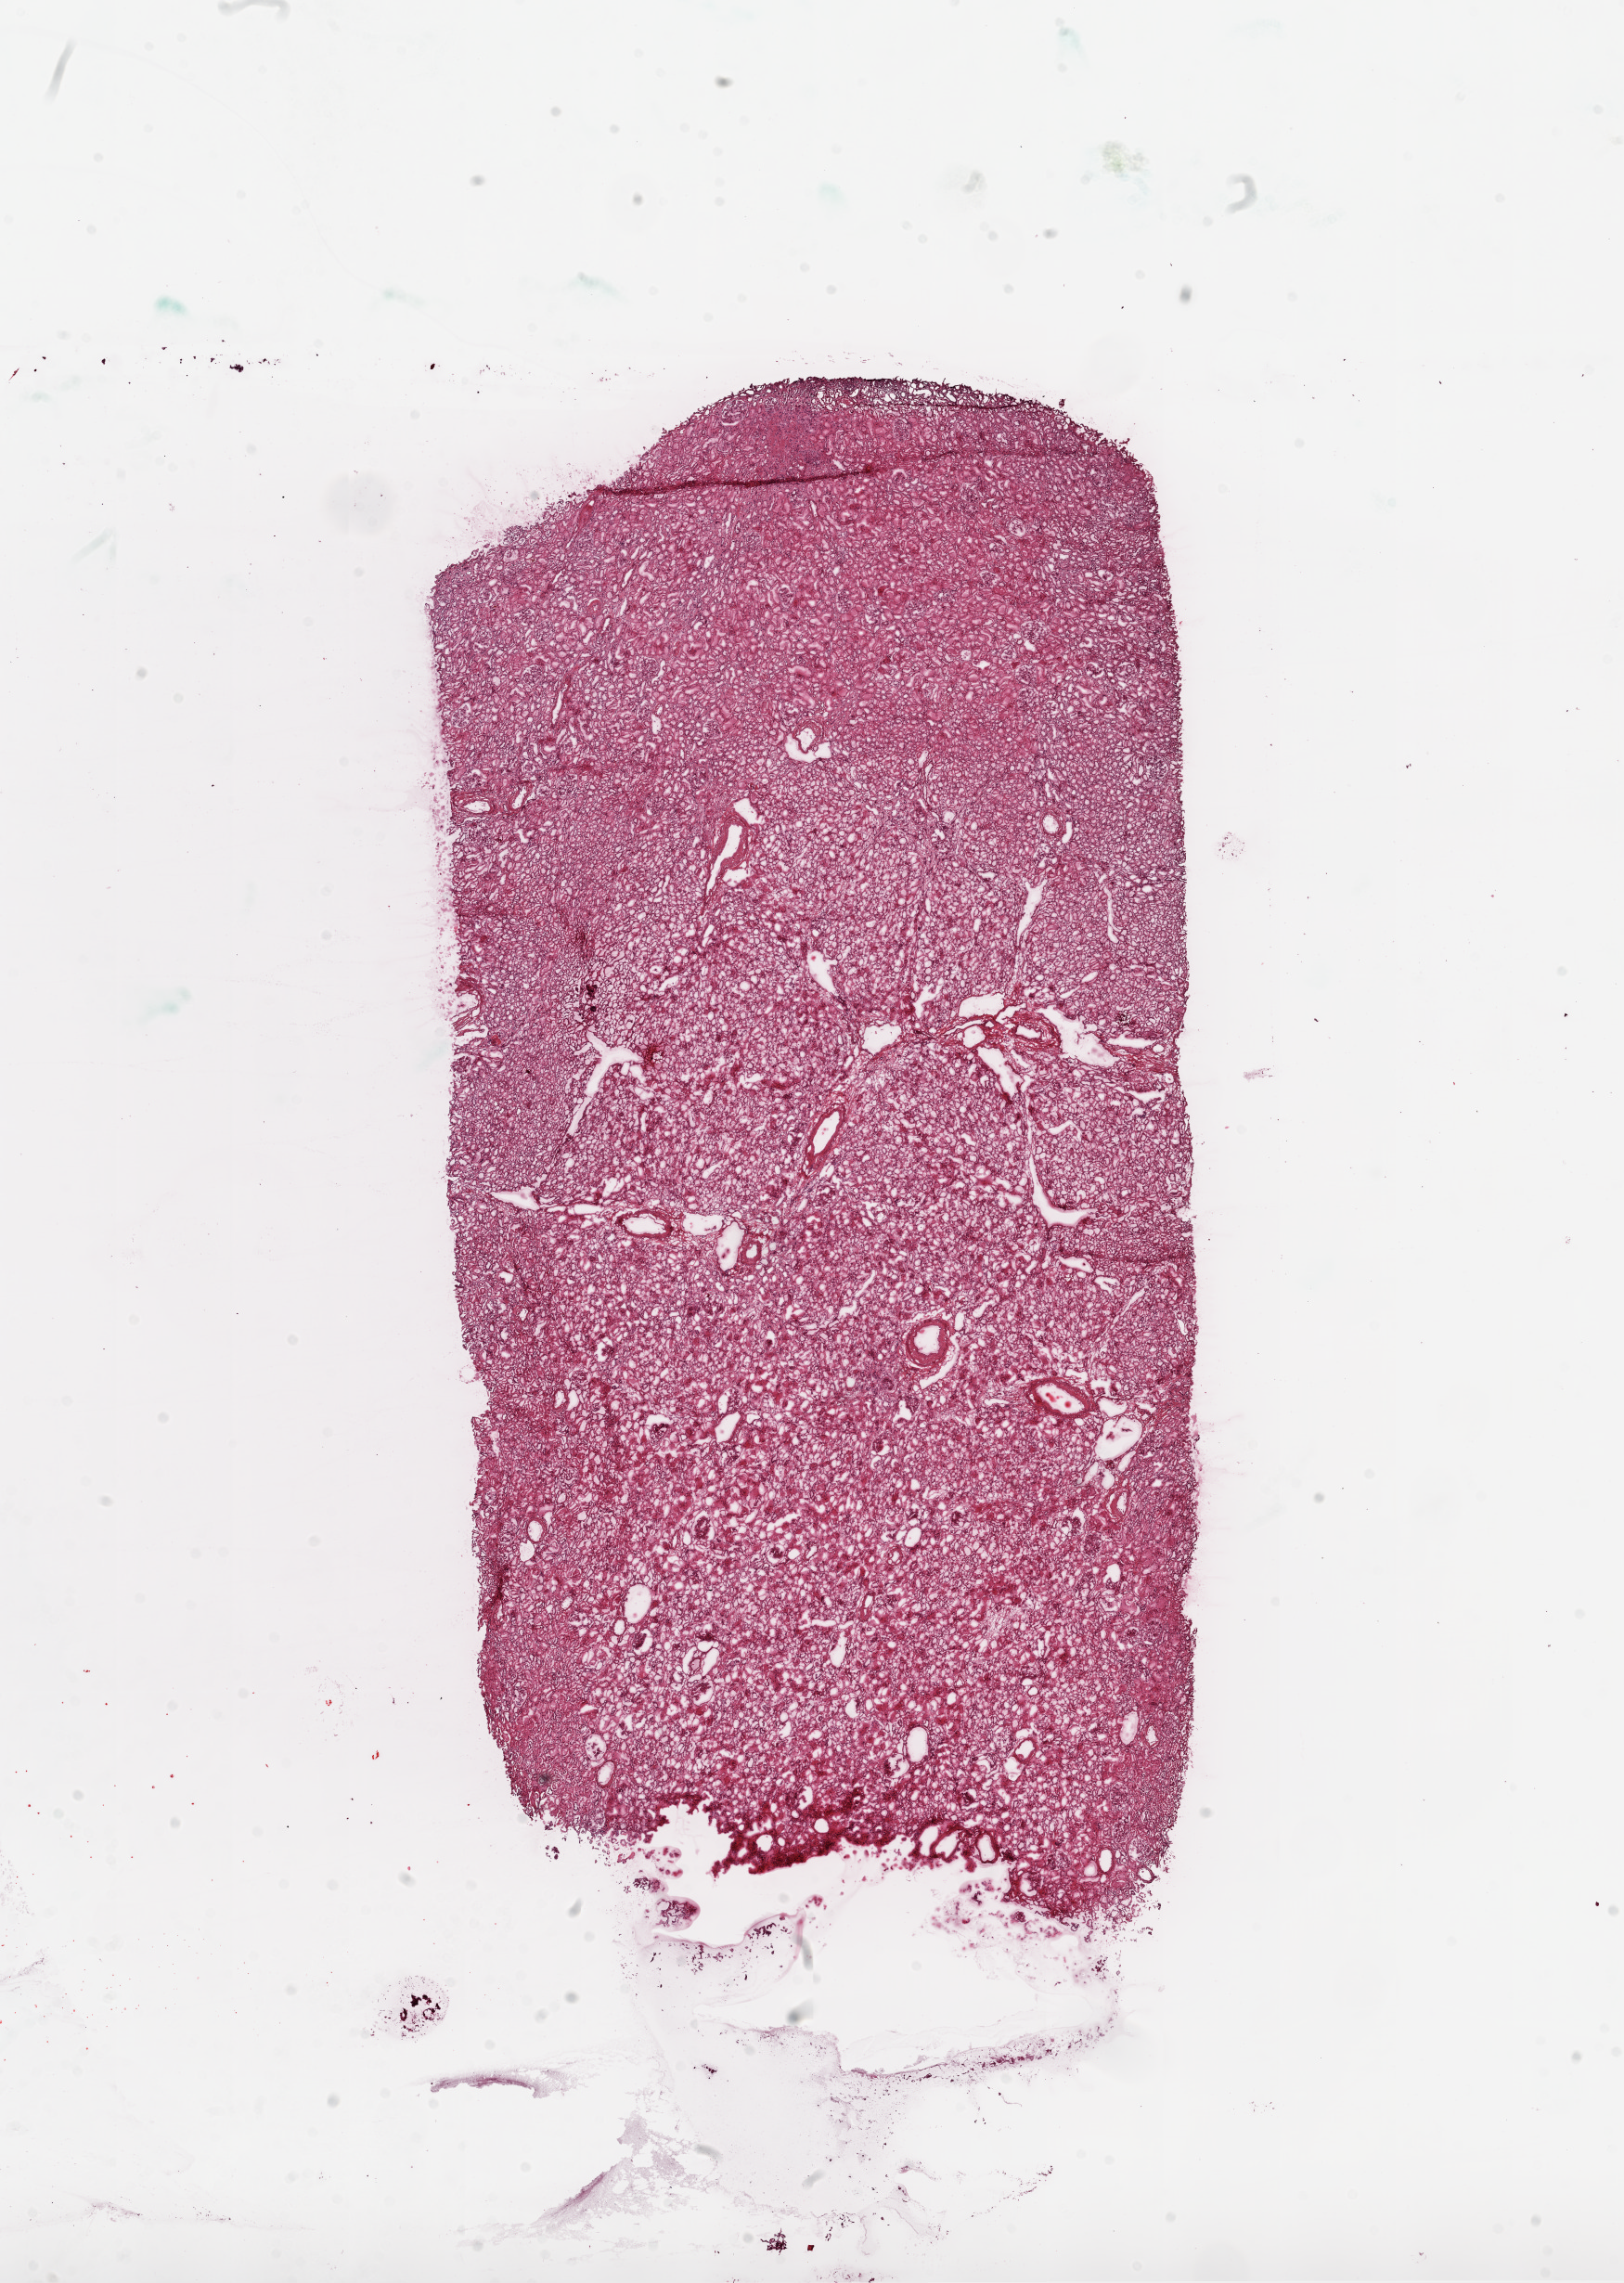
H&E whole-slide image, shown as a low-resolution overview of the whole scanned area (about 14.0 x 19.7 mm, from a 20x scan); frozen section from the top of the tissue portion; kidney, solid tissue normal (non-tumour tissue) sample. Patient: male, age at initial diagnosis 57 years.
This section: solid tissue normal (non-tumour) sample from the same patient. Patient diagnosis: Clear cell adenocarcinoma, NOS.